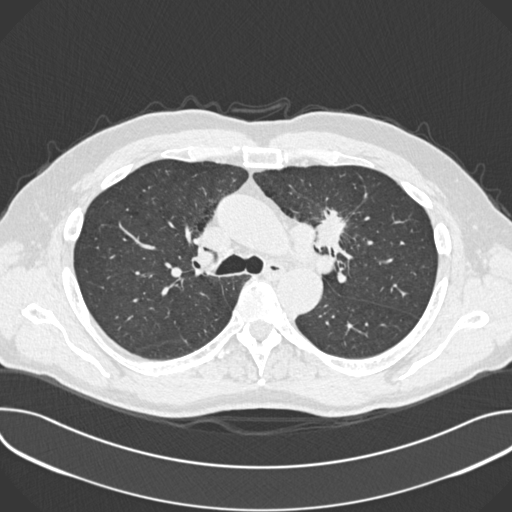
Low-dose screening chest CT, one axial slice; slice 253 of 361 in the series (ordered by position); 120 kVp; lung window (W 1500 / L -600 HU); 1 mm slice thickness; 512 × 512 image matrix, field of view 380 × 380 mm.
Annotated regions visible in this slice (expert manual segmentation):
- lesion 1 (tumor, upper lobe of left lung): bounding box (x1, y1, x2, y2) in pixels: (316, 209, 346, 248)